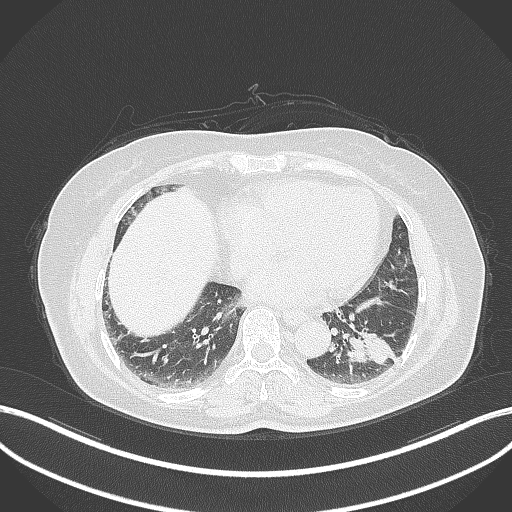
Chest CT, one axial slice; slice 135 of 311 in the series (ordered by position); reconstruction kernel B70f; 120 kVp; lung window (W 1500 / L -600 HU); 1 mm slice thickness; 512 × 512 image matrix, field of view 400 × 400 mm. Patient: female, 59 years. Case-level facts recorded for this patient, not image findings: clinical TNM (as recorded): T2a N0 M0; histopathological grade: G2-3.
Outlined on this slice (bounding box drawn by a radiologist):
- lung tumour (recorded histology: adenocarcinoma): bounding box [x1, y1, x2, y2] px = [344, 321, 397, 371]